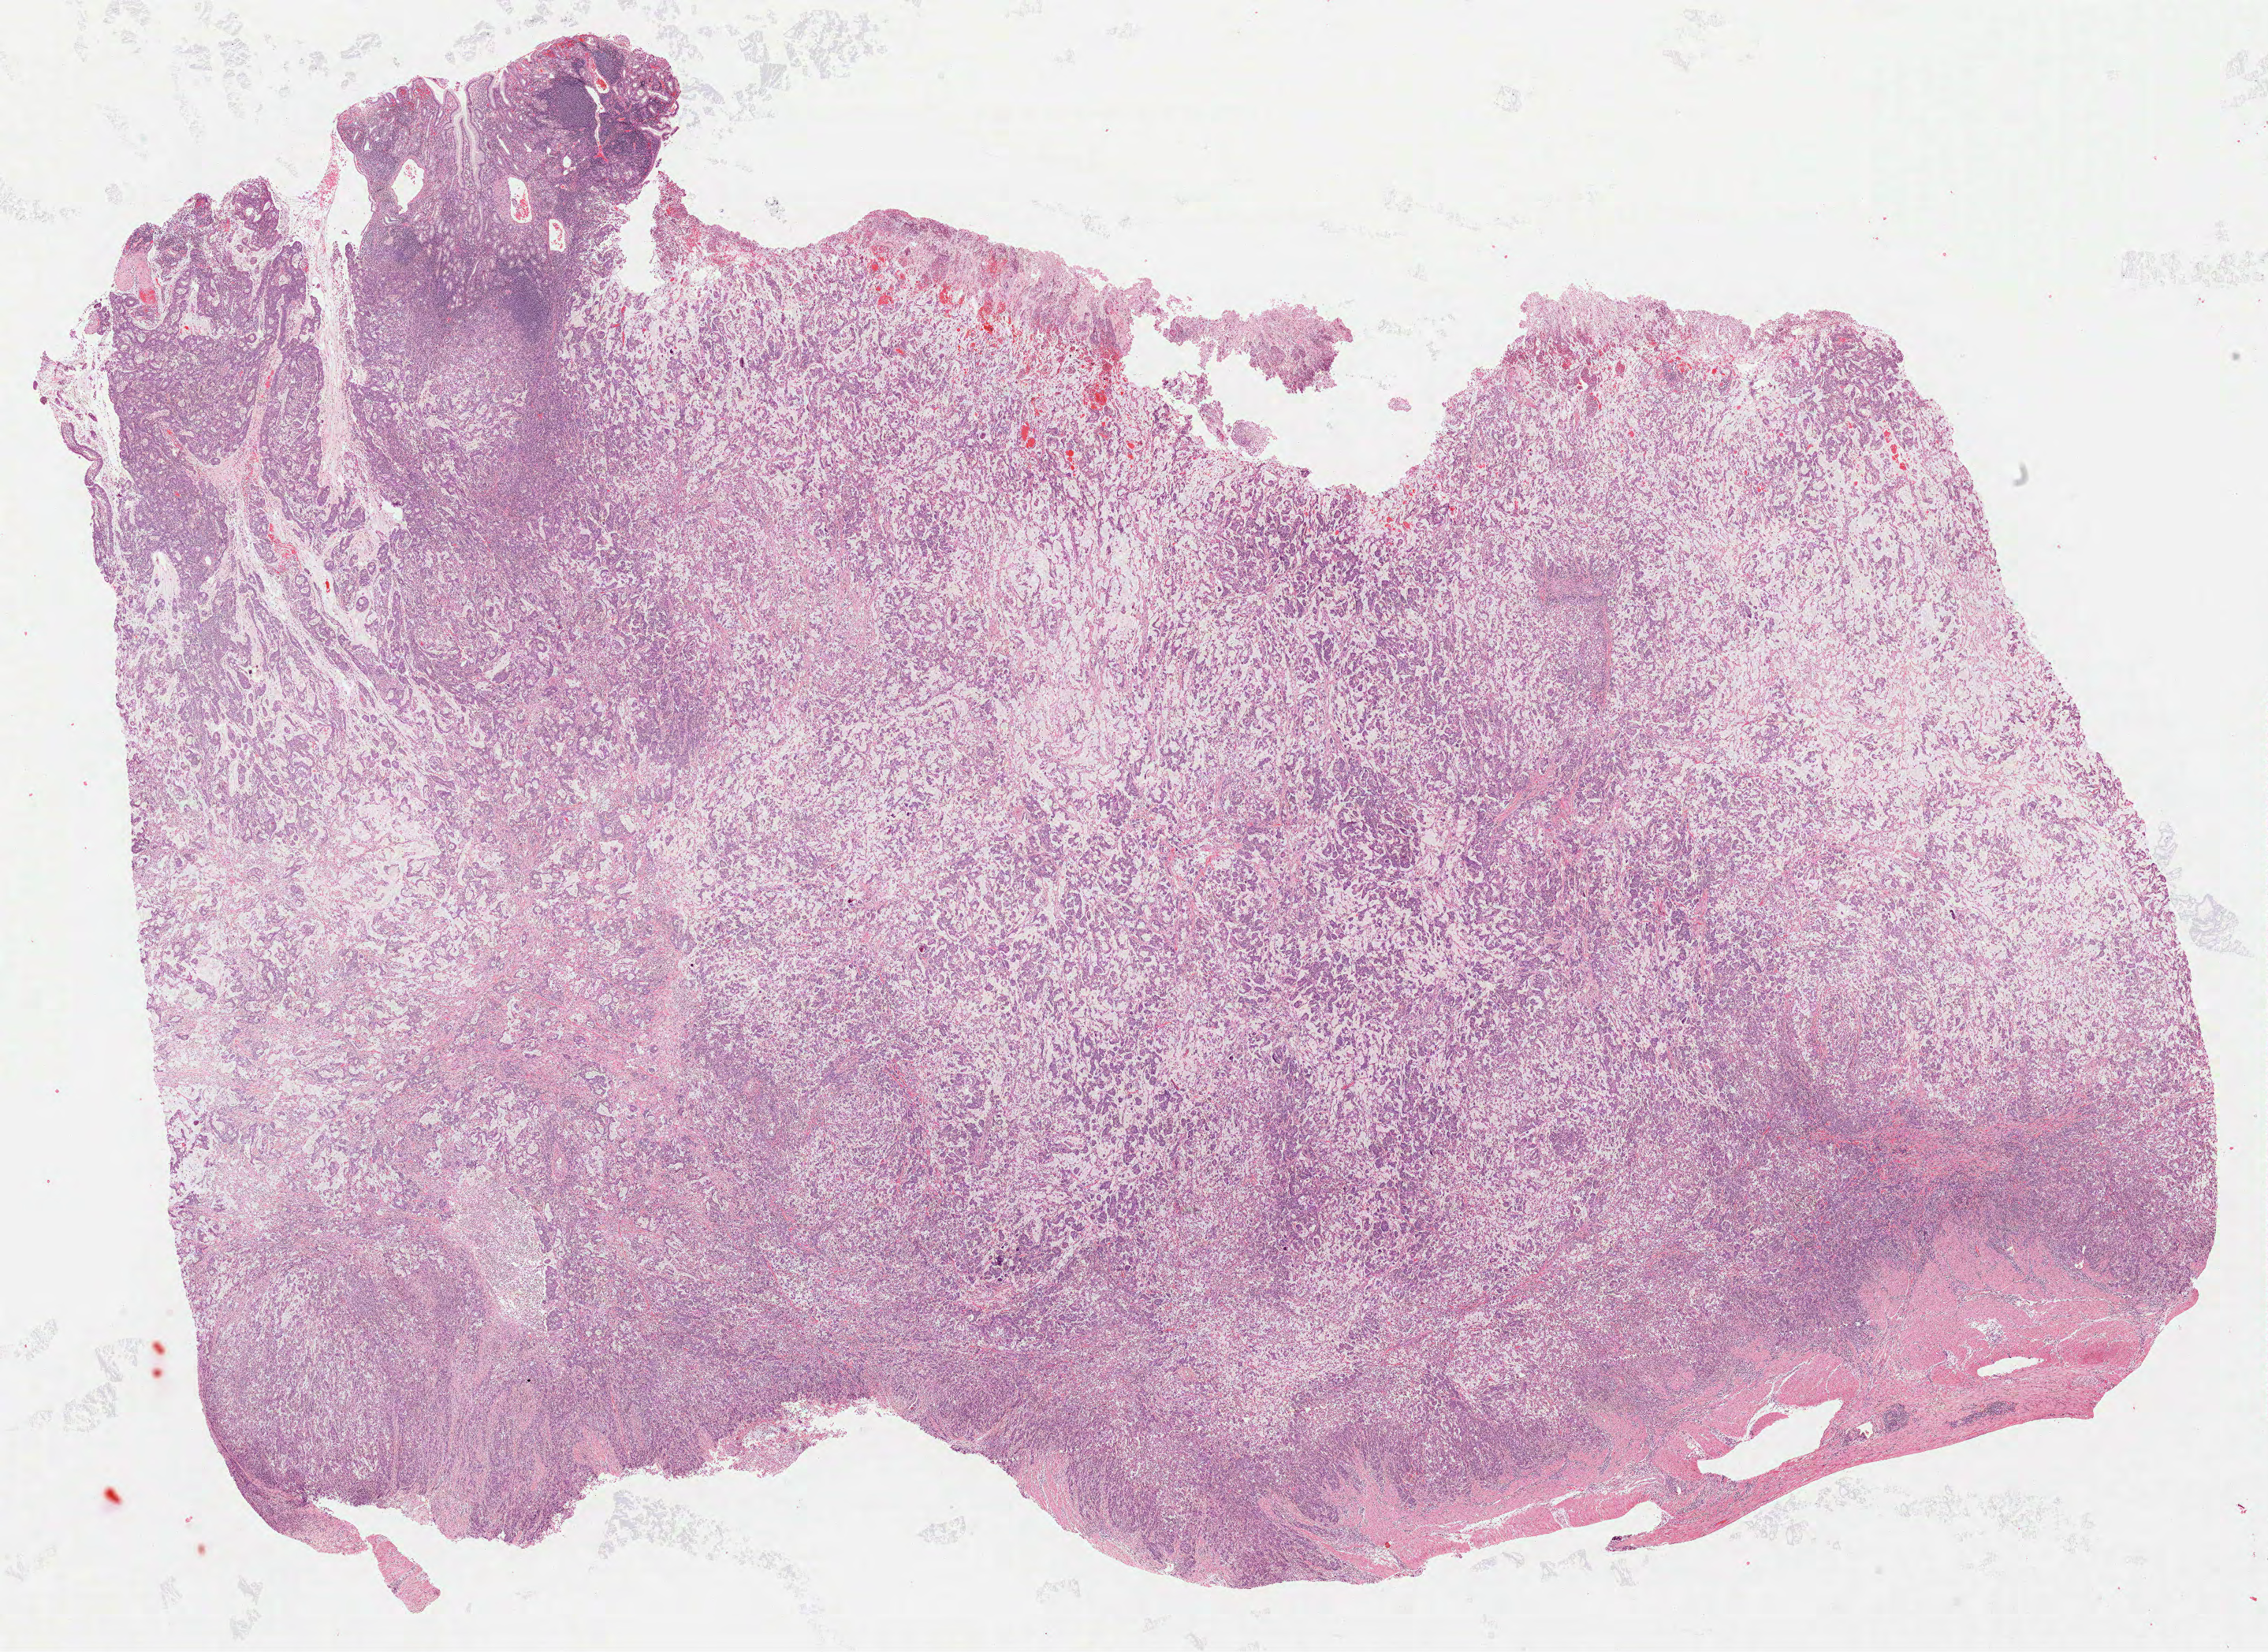
H&E whole-slide image, low-resolution overview of the scanned area, about 23.2 x 16.9 mm (acquisition: 40x scan). FFPE section. Primary tumour sample from the stomach. Patient: female, age at initial diagnosis 64 years. Histologic grade: G3 (poorly differentiated).
TNM: T3 N0 M0. AJCC pathologic stage: IIA. Pathologic diagnosis: Adenocarcinoma, NOS (body of stomach). Lymph nodes positive (case pathology): 0 of 3 examined.